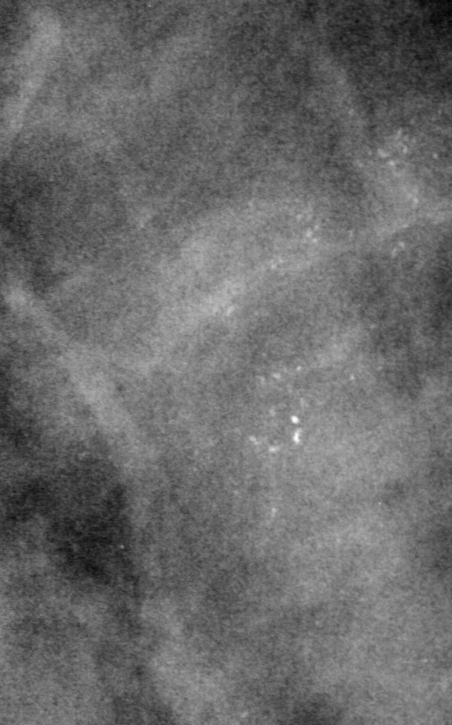
Cropped region of a digitized screen-film mammogram centred on a radiologist-marked abnormality, right breast, MLO view, BI-RADS breast density category 4 (scale 1–4).
Calcifications, morphology pleomorphic, distribution clustered; BI-RADS assessment category 0 (incomplete: needs additional imaging); subtlety rating 4 on a 1 (subtle) to 5 (obvious) scale; pathology result (as recorded, not read from the image): malignant.